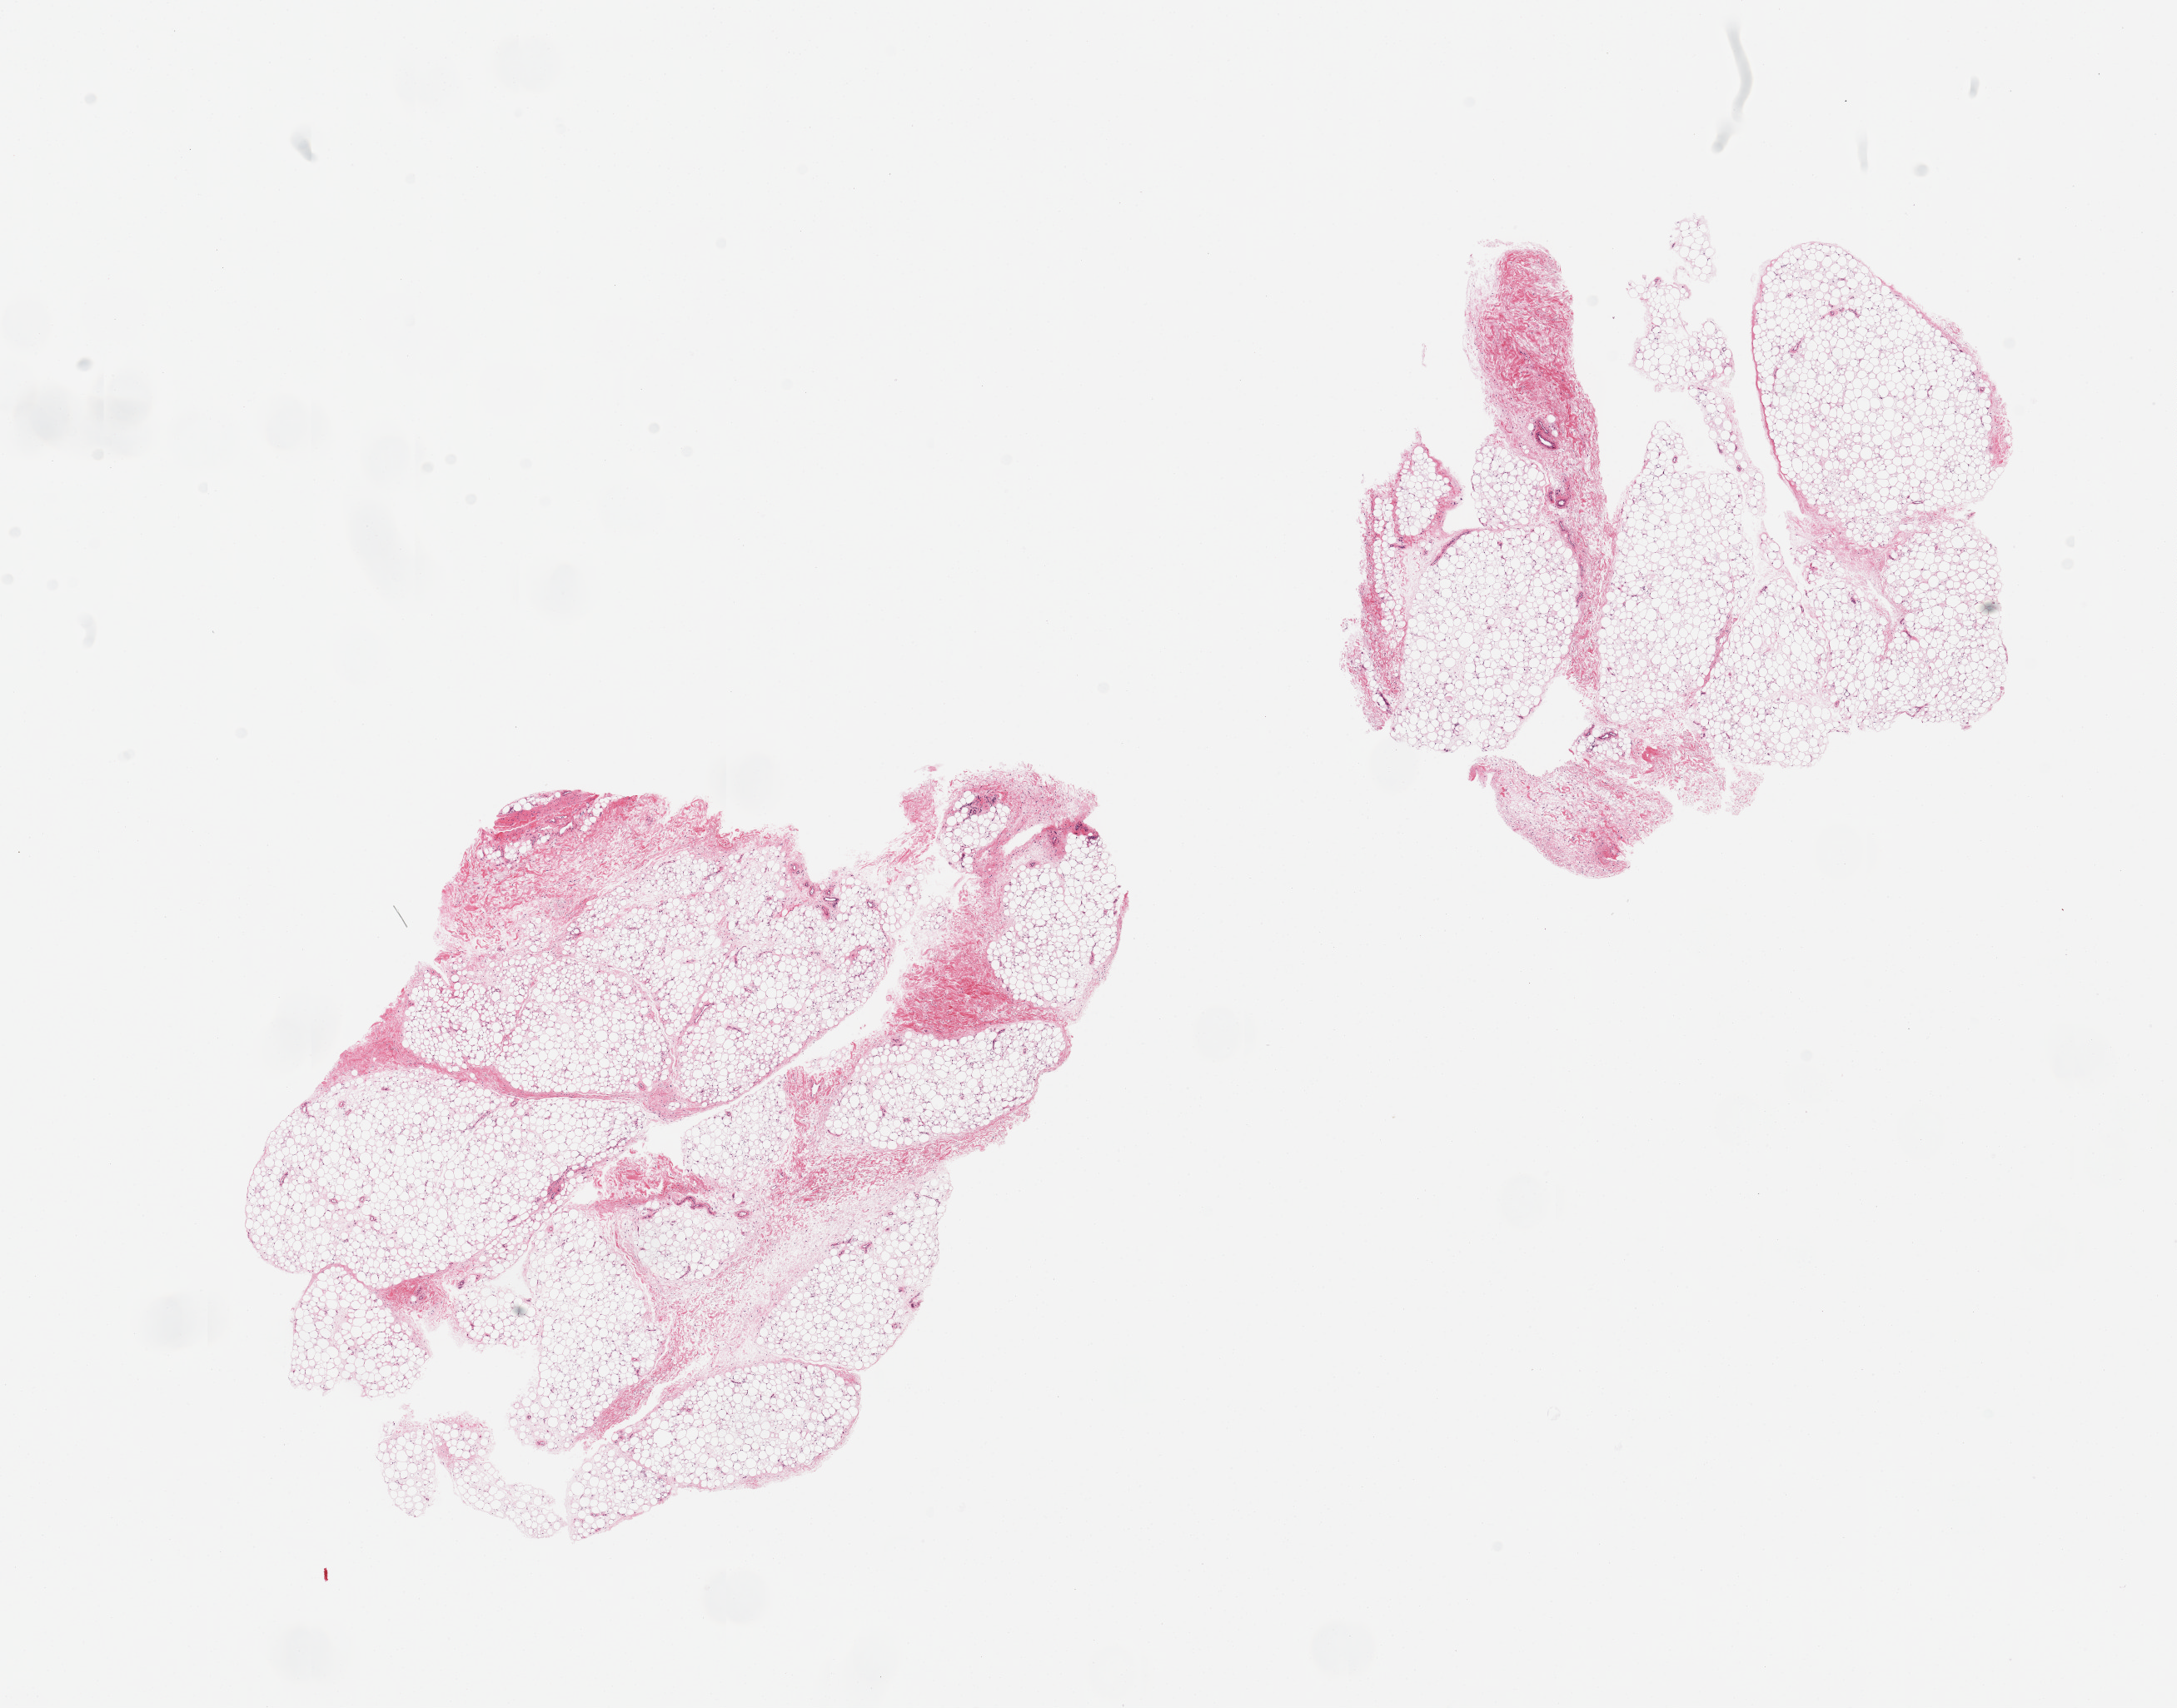
H&E whole-slide image, brightfield — a low-resolution overview of the entire scanned area, about 20.7 x 16.2 mm. PAXgene-fixed, paraffin-embedded tissue. Sampled site (target tissue): adipose tissue. Donor tissue sample. Donor sex: male.
- reviewer comment on this tissue sample: 2 pieces; Fascia is ~10 %